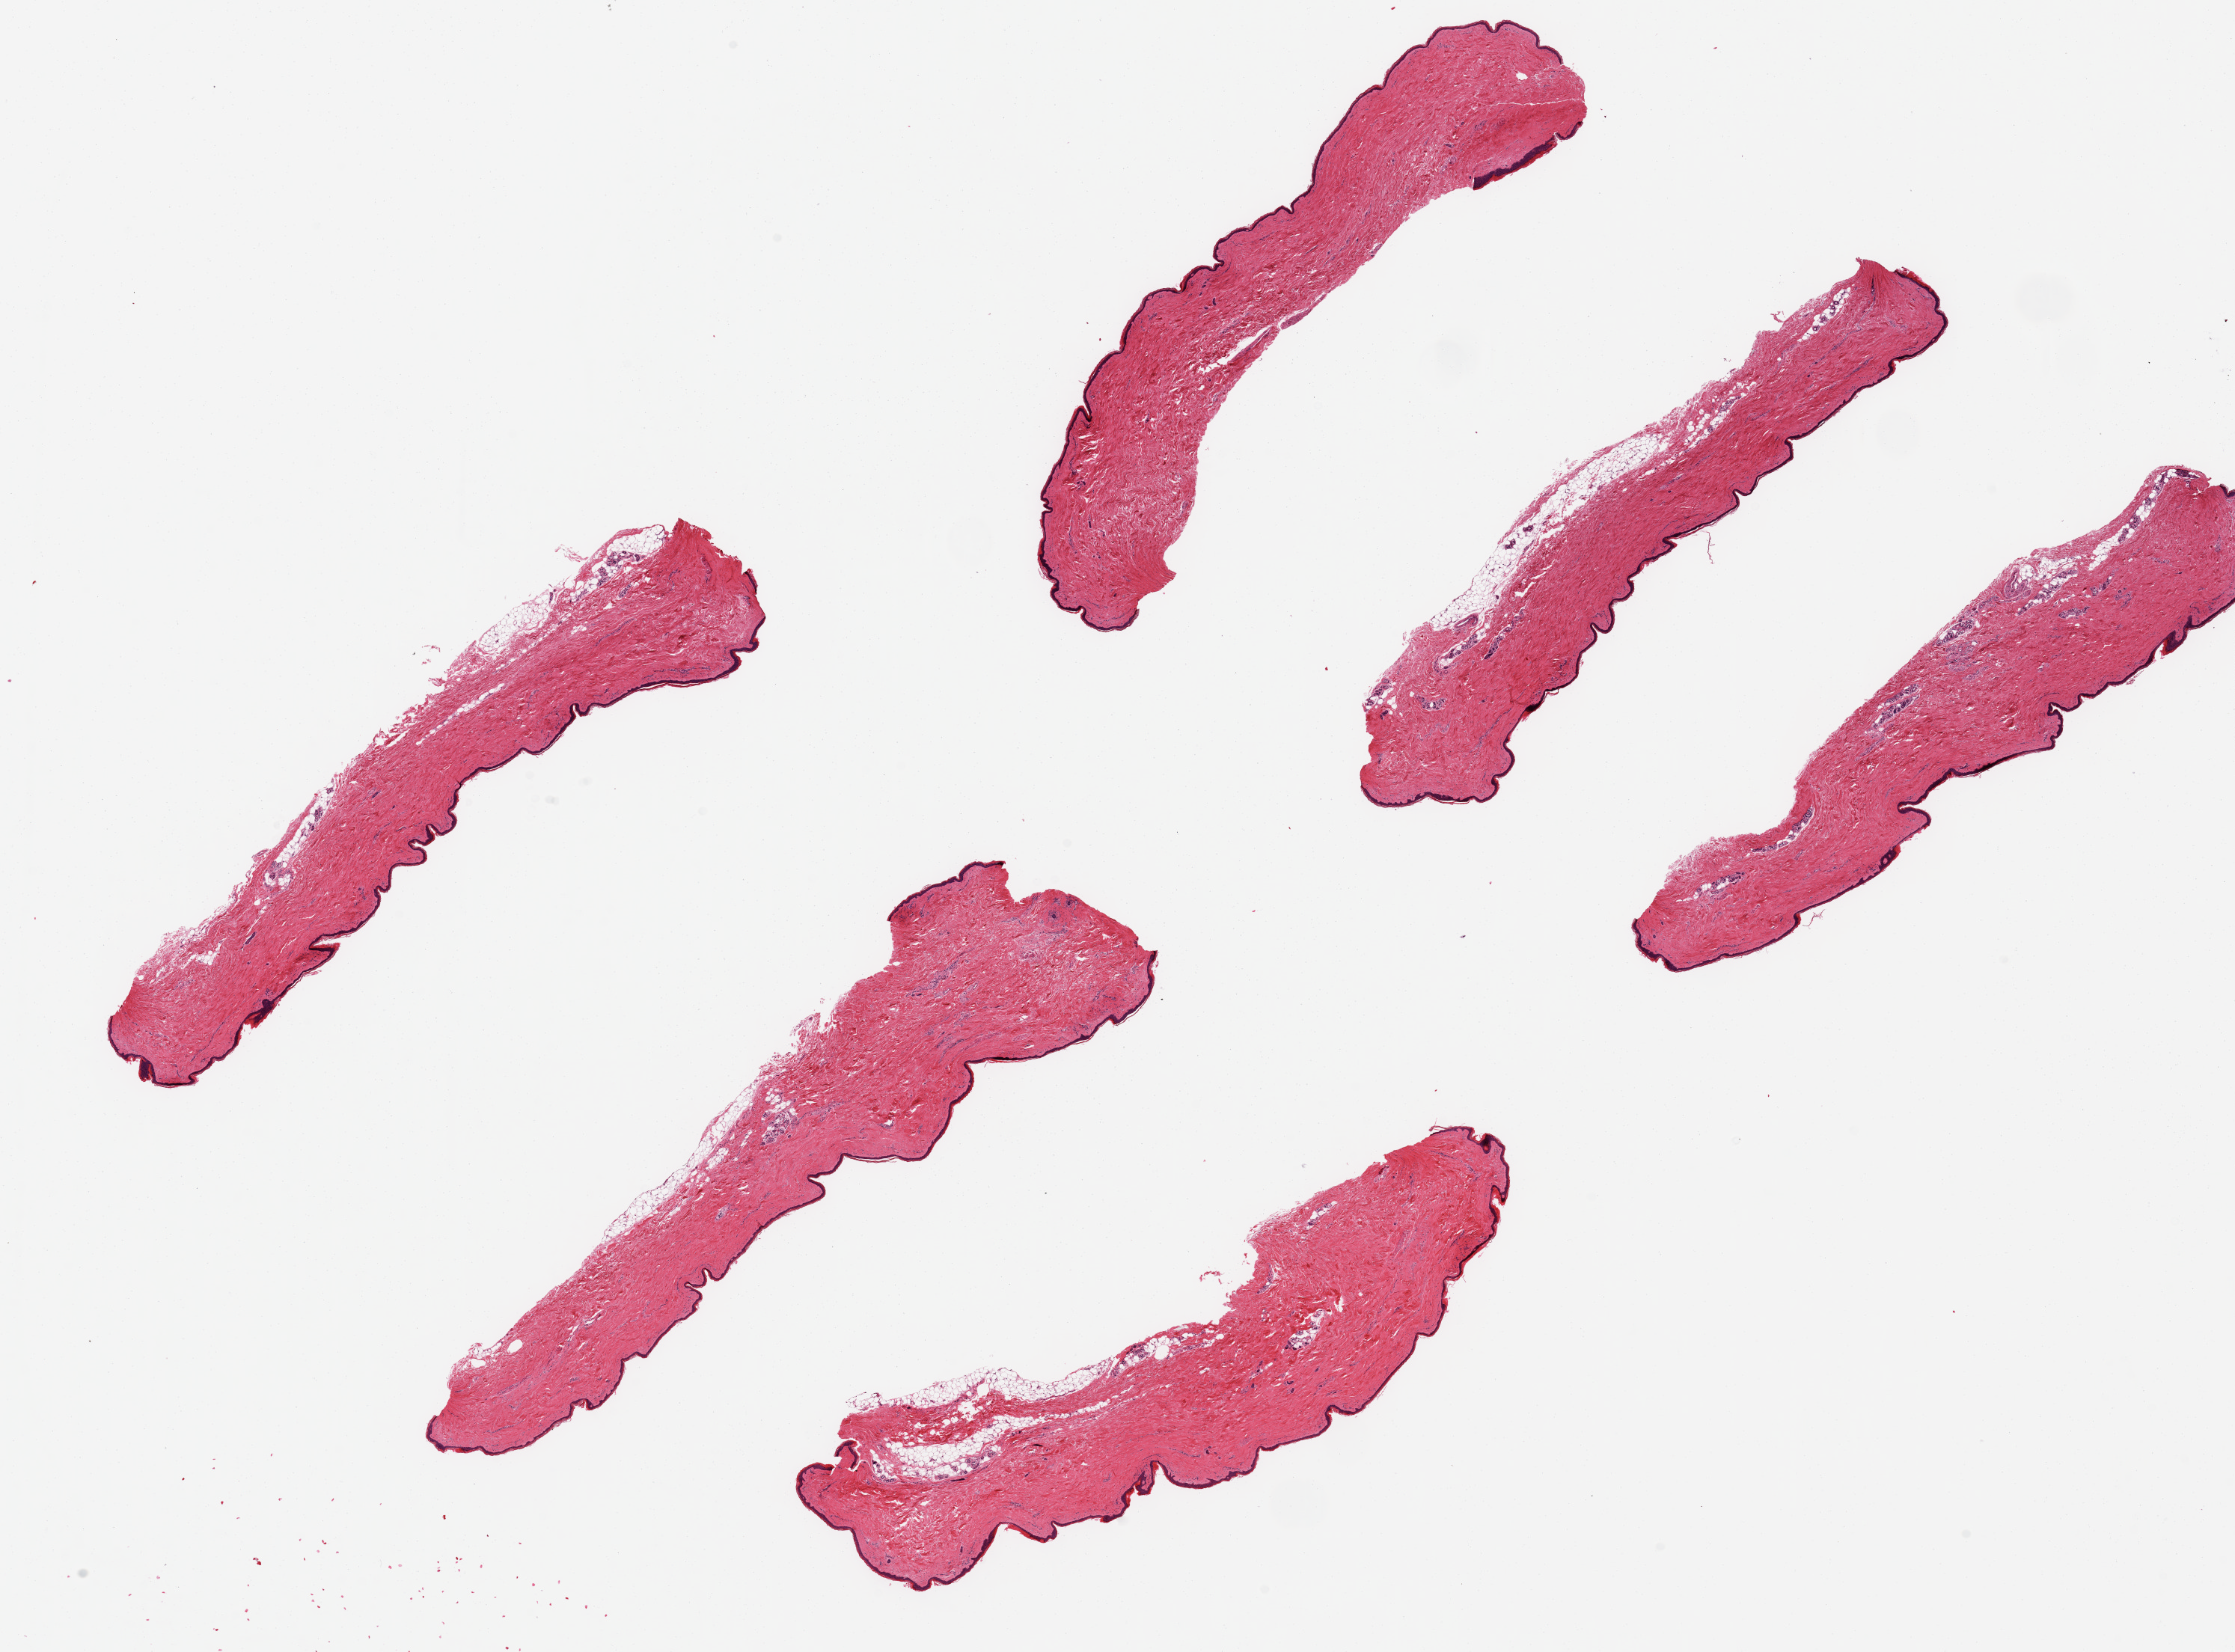
Whole-slide image, haematoxylin and eosin stain, whole scanned area (about 23.6 x 17.5 mm) shown as a low-resolution overview; PAXgene-fixed, paraffin-embedded tissue; target tissue: skin of lower leg; tissue donor sample. Female donor.
Pathologist's review note for this sample: 6 ~8x1.5mm pieces. Squamous mucosa is 1.5-2% of thickness.